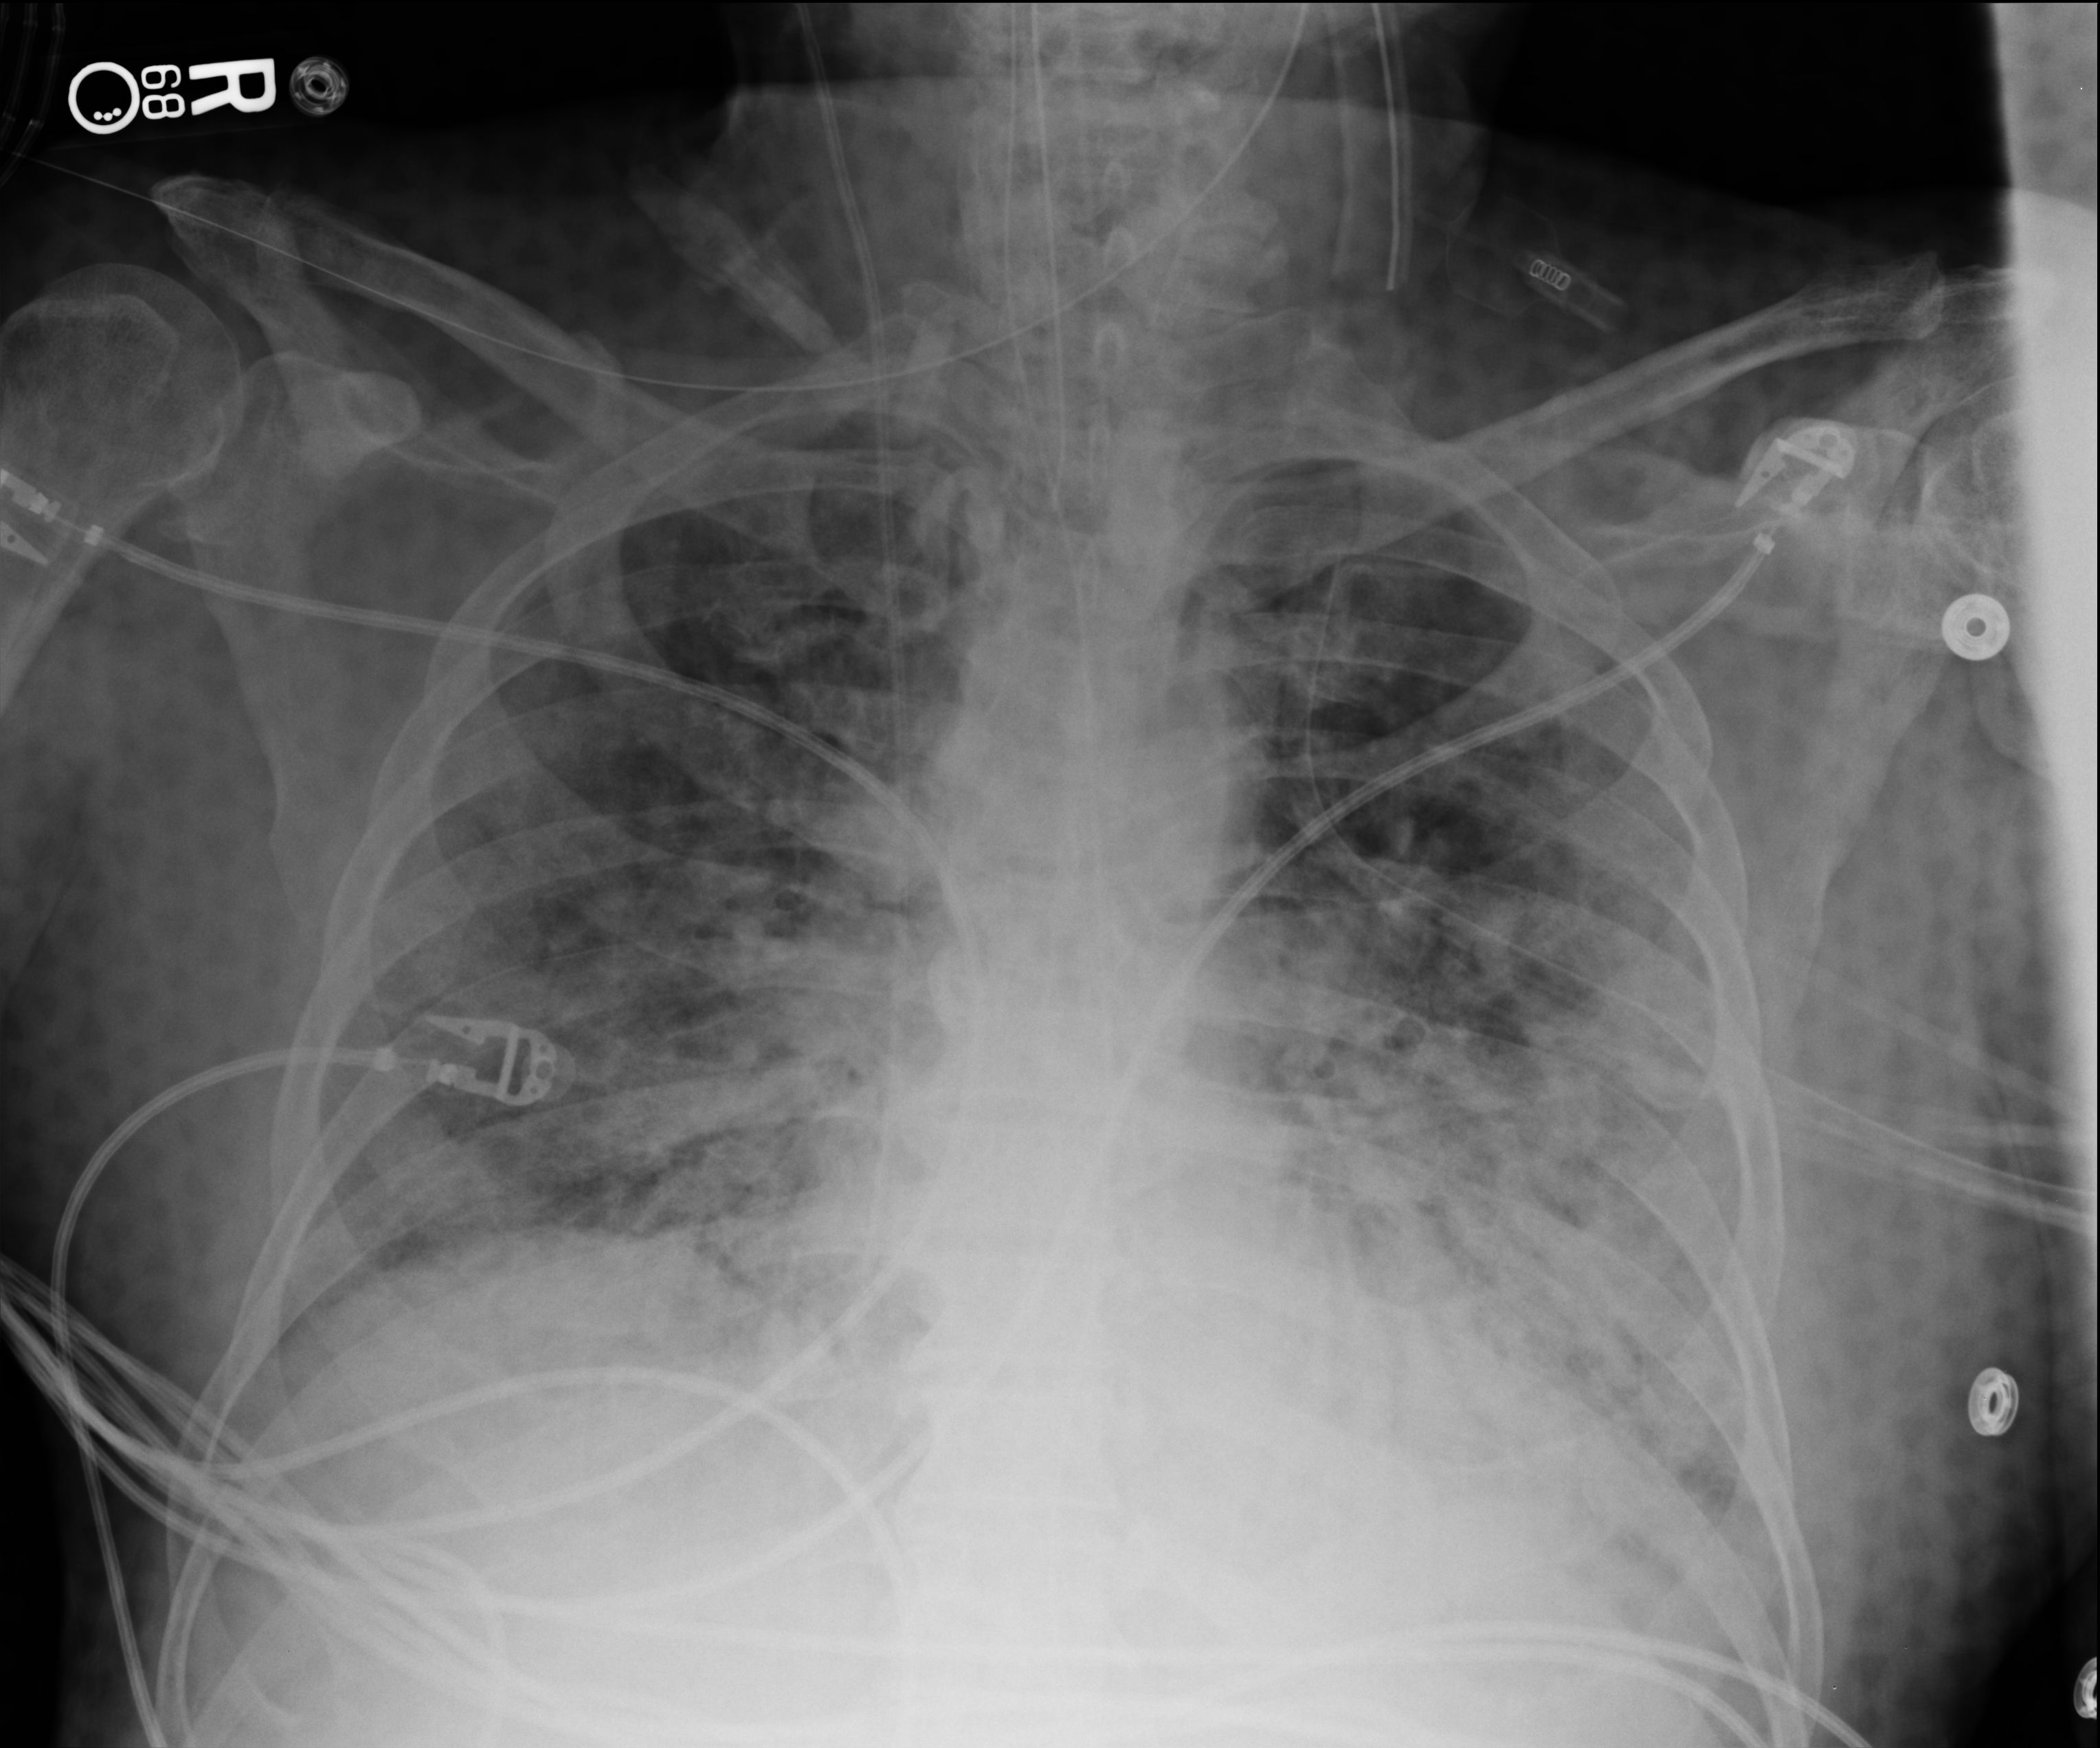
Bedside chest radiograph (computed radiography). Male patient hospitalised with COVID-19, age 75–90 years.
Admission-level facts for this patient (not findings on this image; timing relative to this image not recorded): COPD (admission record): no.